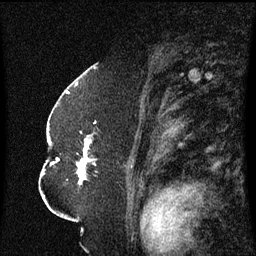
Breast MRI (dynamic contrast-enhanced), one sagittal slice; dynamic contrast-enhanced series, image 2 of 3 at this slice position (ordered by acquisition); 1.5 T; TE 4.2 ms, TR 8.4 ms; 256 × 256 image matrix, field of view 200 × 200 mm. Patient: female, 52 years. Case-level facts recorded for this patient, not image findings: setting: breast cancer imaged before/during neoadjuvant chemotherapy; receptor status: HR-positive, HER2-negative.
Annotated regions visible in this slice (semi-automatic segmentation, software-assisted and operator-edited):
- analysis volume of interest (the breast-tissue region the enhancement analysis was run in; not a lesion): bounding box [x1, y1, x2, y2] px = [49, 124, 98, 185]
- tumour enhancement mask (voxels above the 70 % enhancement threshold inside the analysis volume of interest): [57, 140, 92, 183]